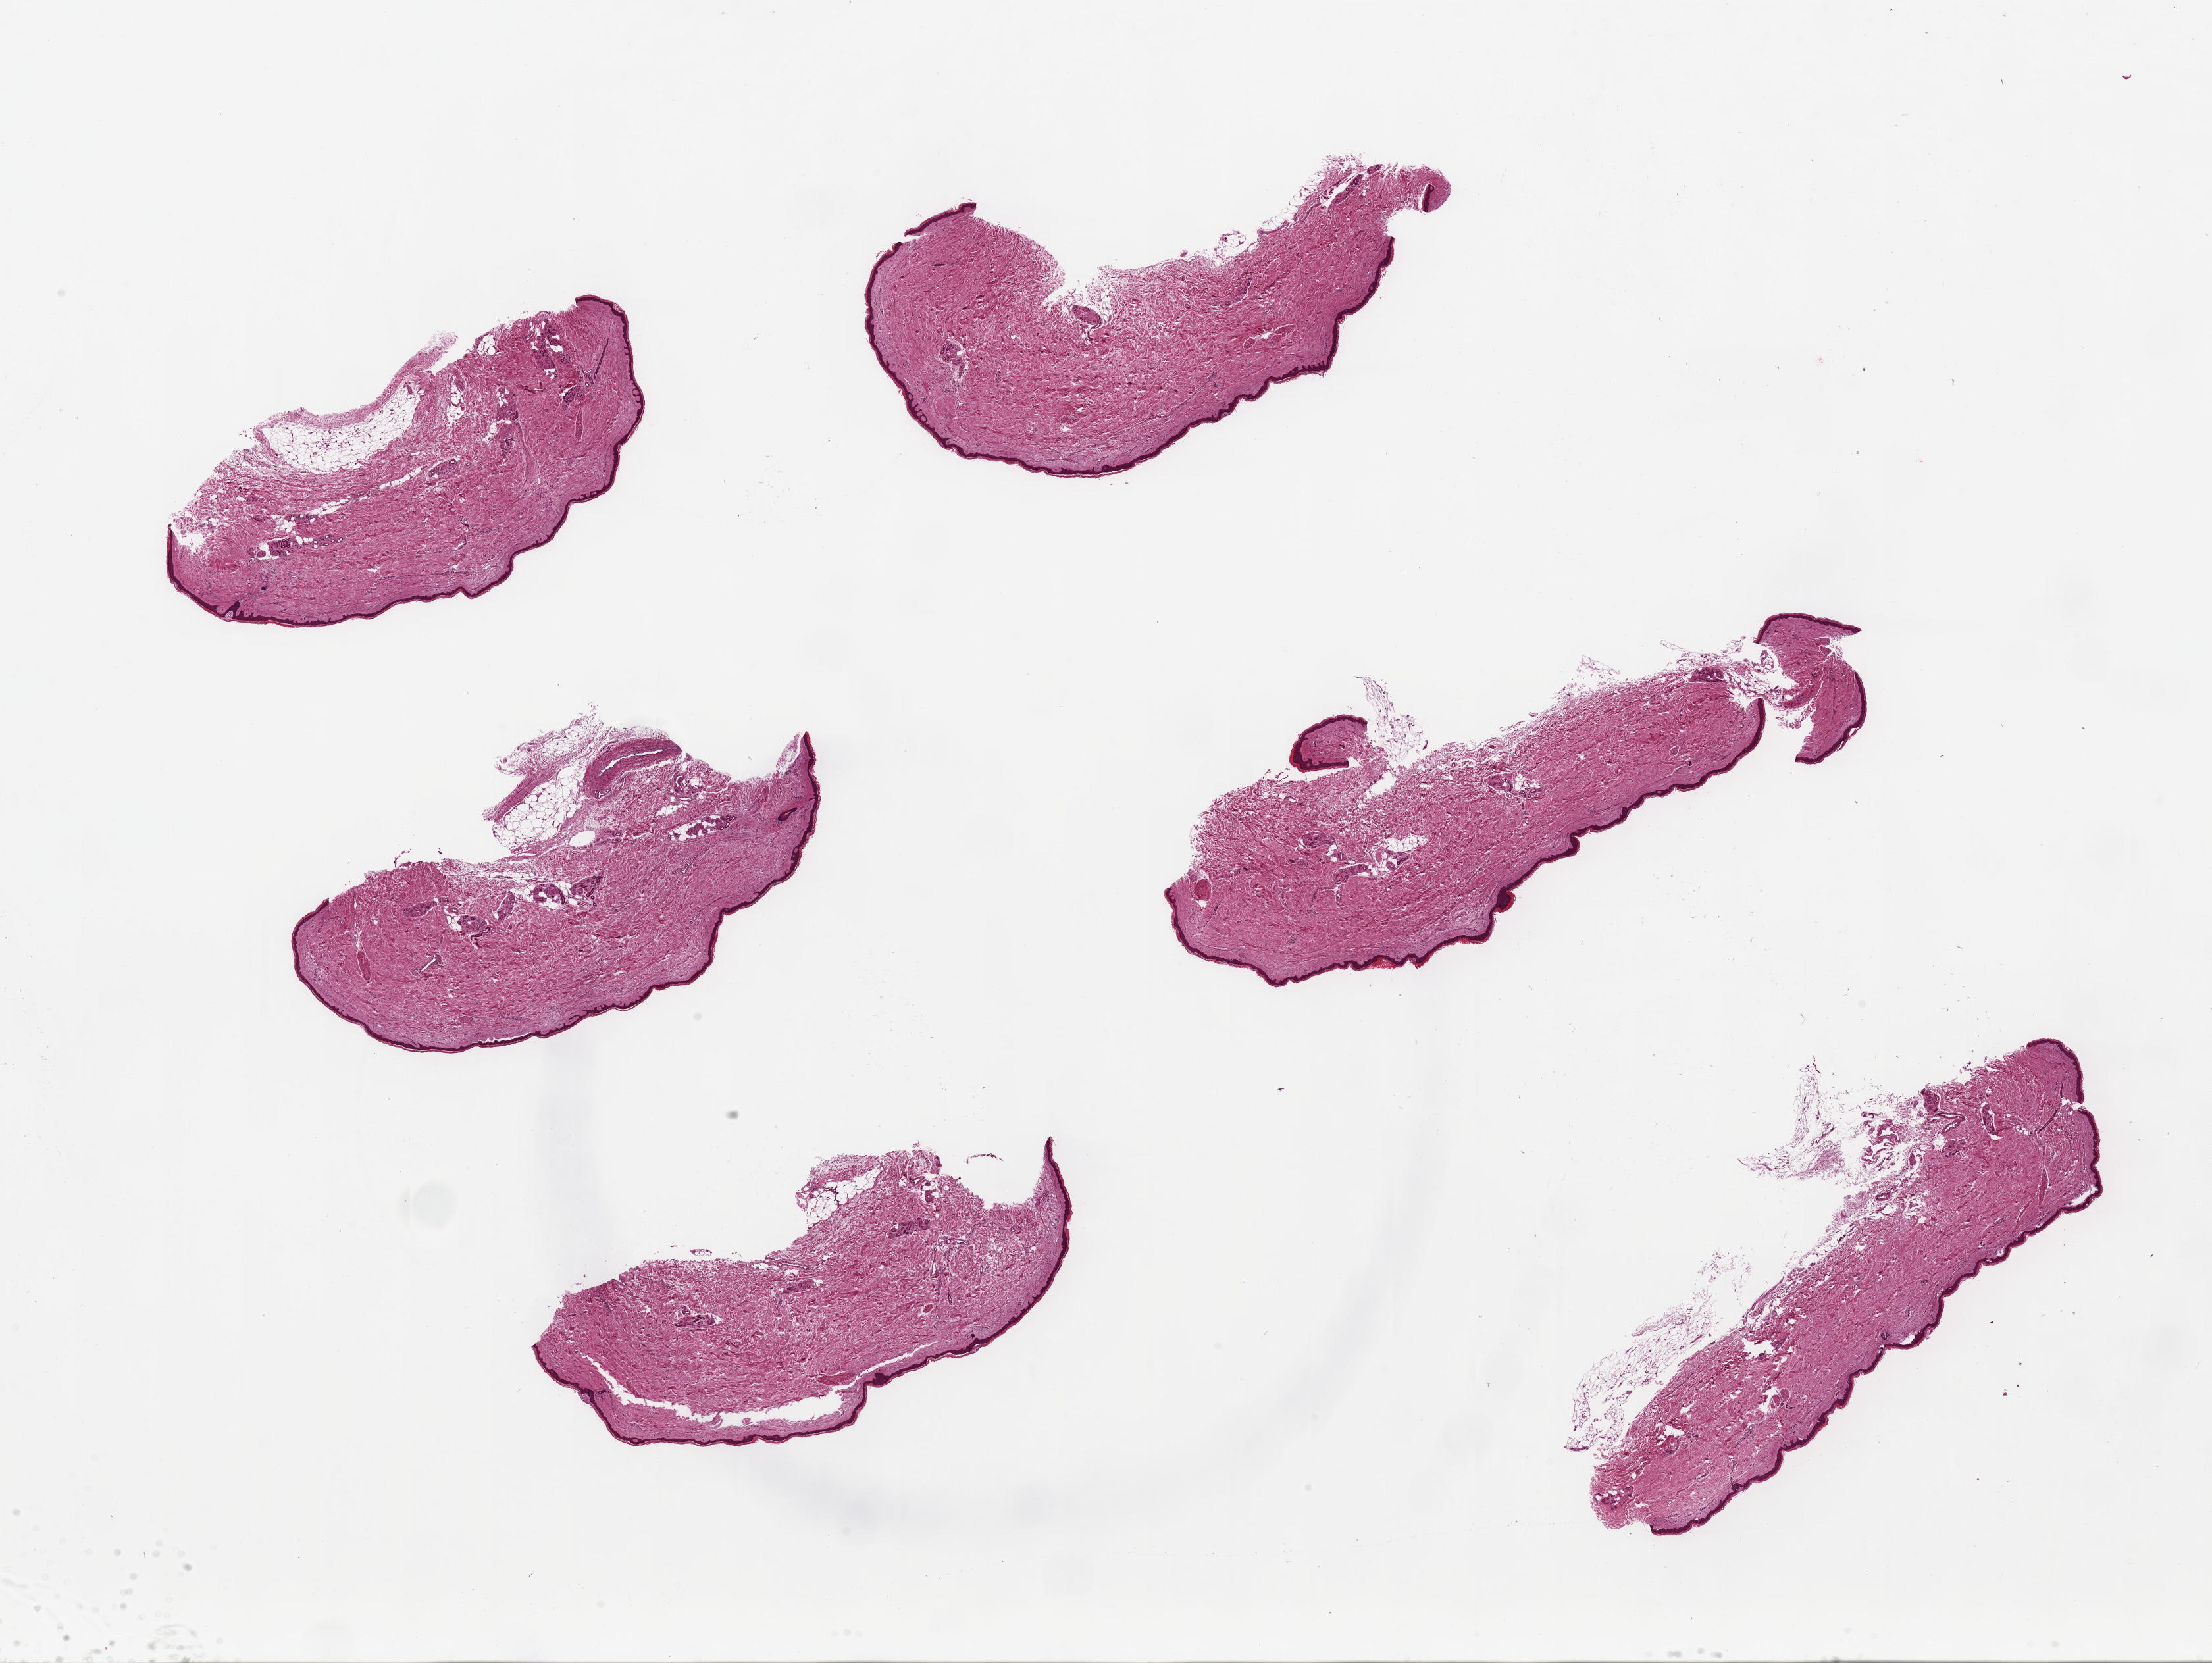
Whole-slide image, haematoxylin and eosin stain — a low-resolution overview of the entire scanned area, about 26.6 x 20.0 mm. PAXgene-fixed, paraffin-embedded tissue. Target tissue: skin of lower leg. Donor tissue sample. Male donor.
Reviewer comment on this tissue sample: 6 ~5-8x2.5mm pieces. Squamous epithelium is ~2% of specimen thickness.